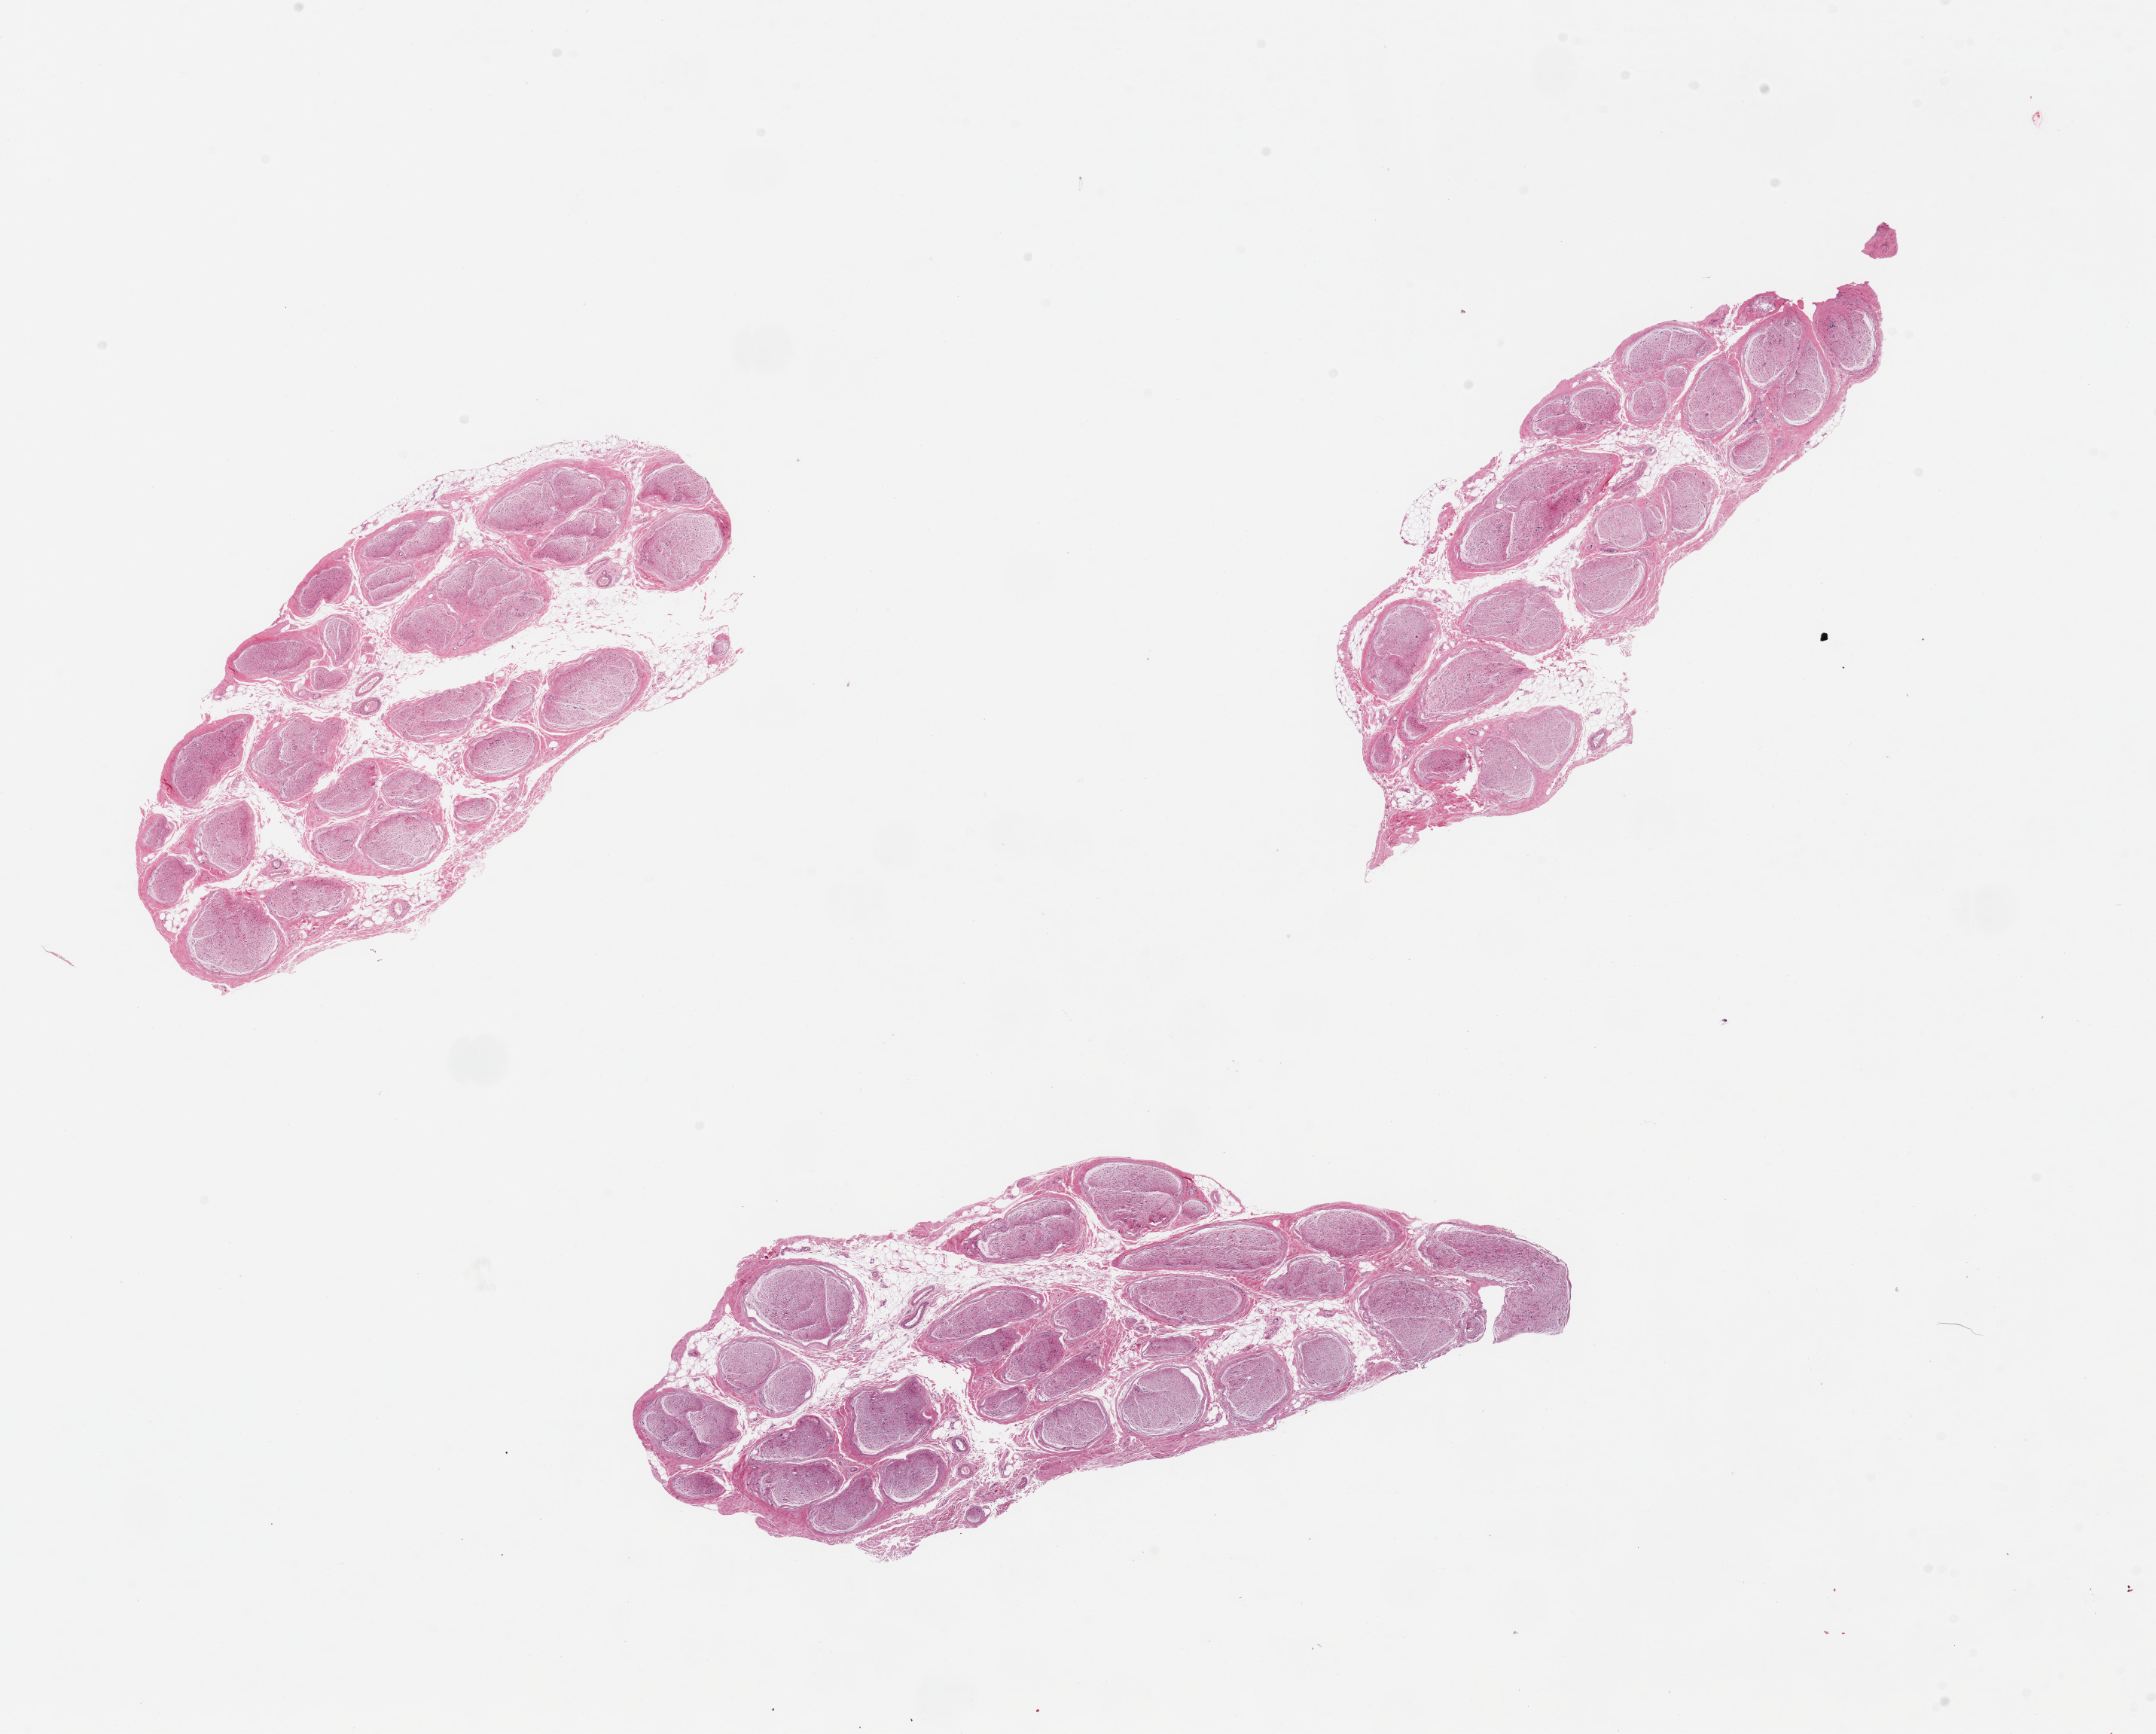
Hematoxylin and eosin (H&E) whole-slide image, shown as a low-resolution overview of the whole scanned area (about 22.6 x 18.2 mm, from a 20x scan). PAXgene-fixed, paraffin-embedded tissue. Section of tibial nerve (target tissue). Tissue donor sample. Donor: male.
- review note (as recorded): 3 pieces; 10% internal fat content